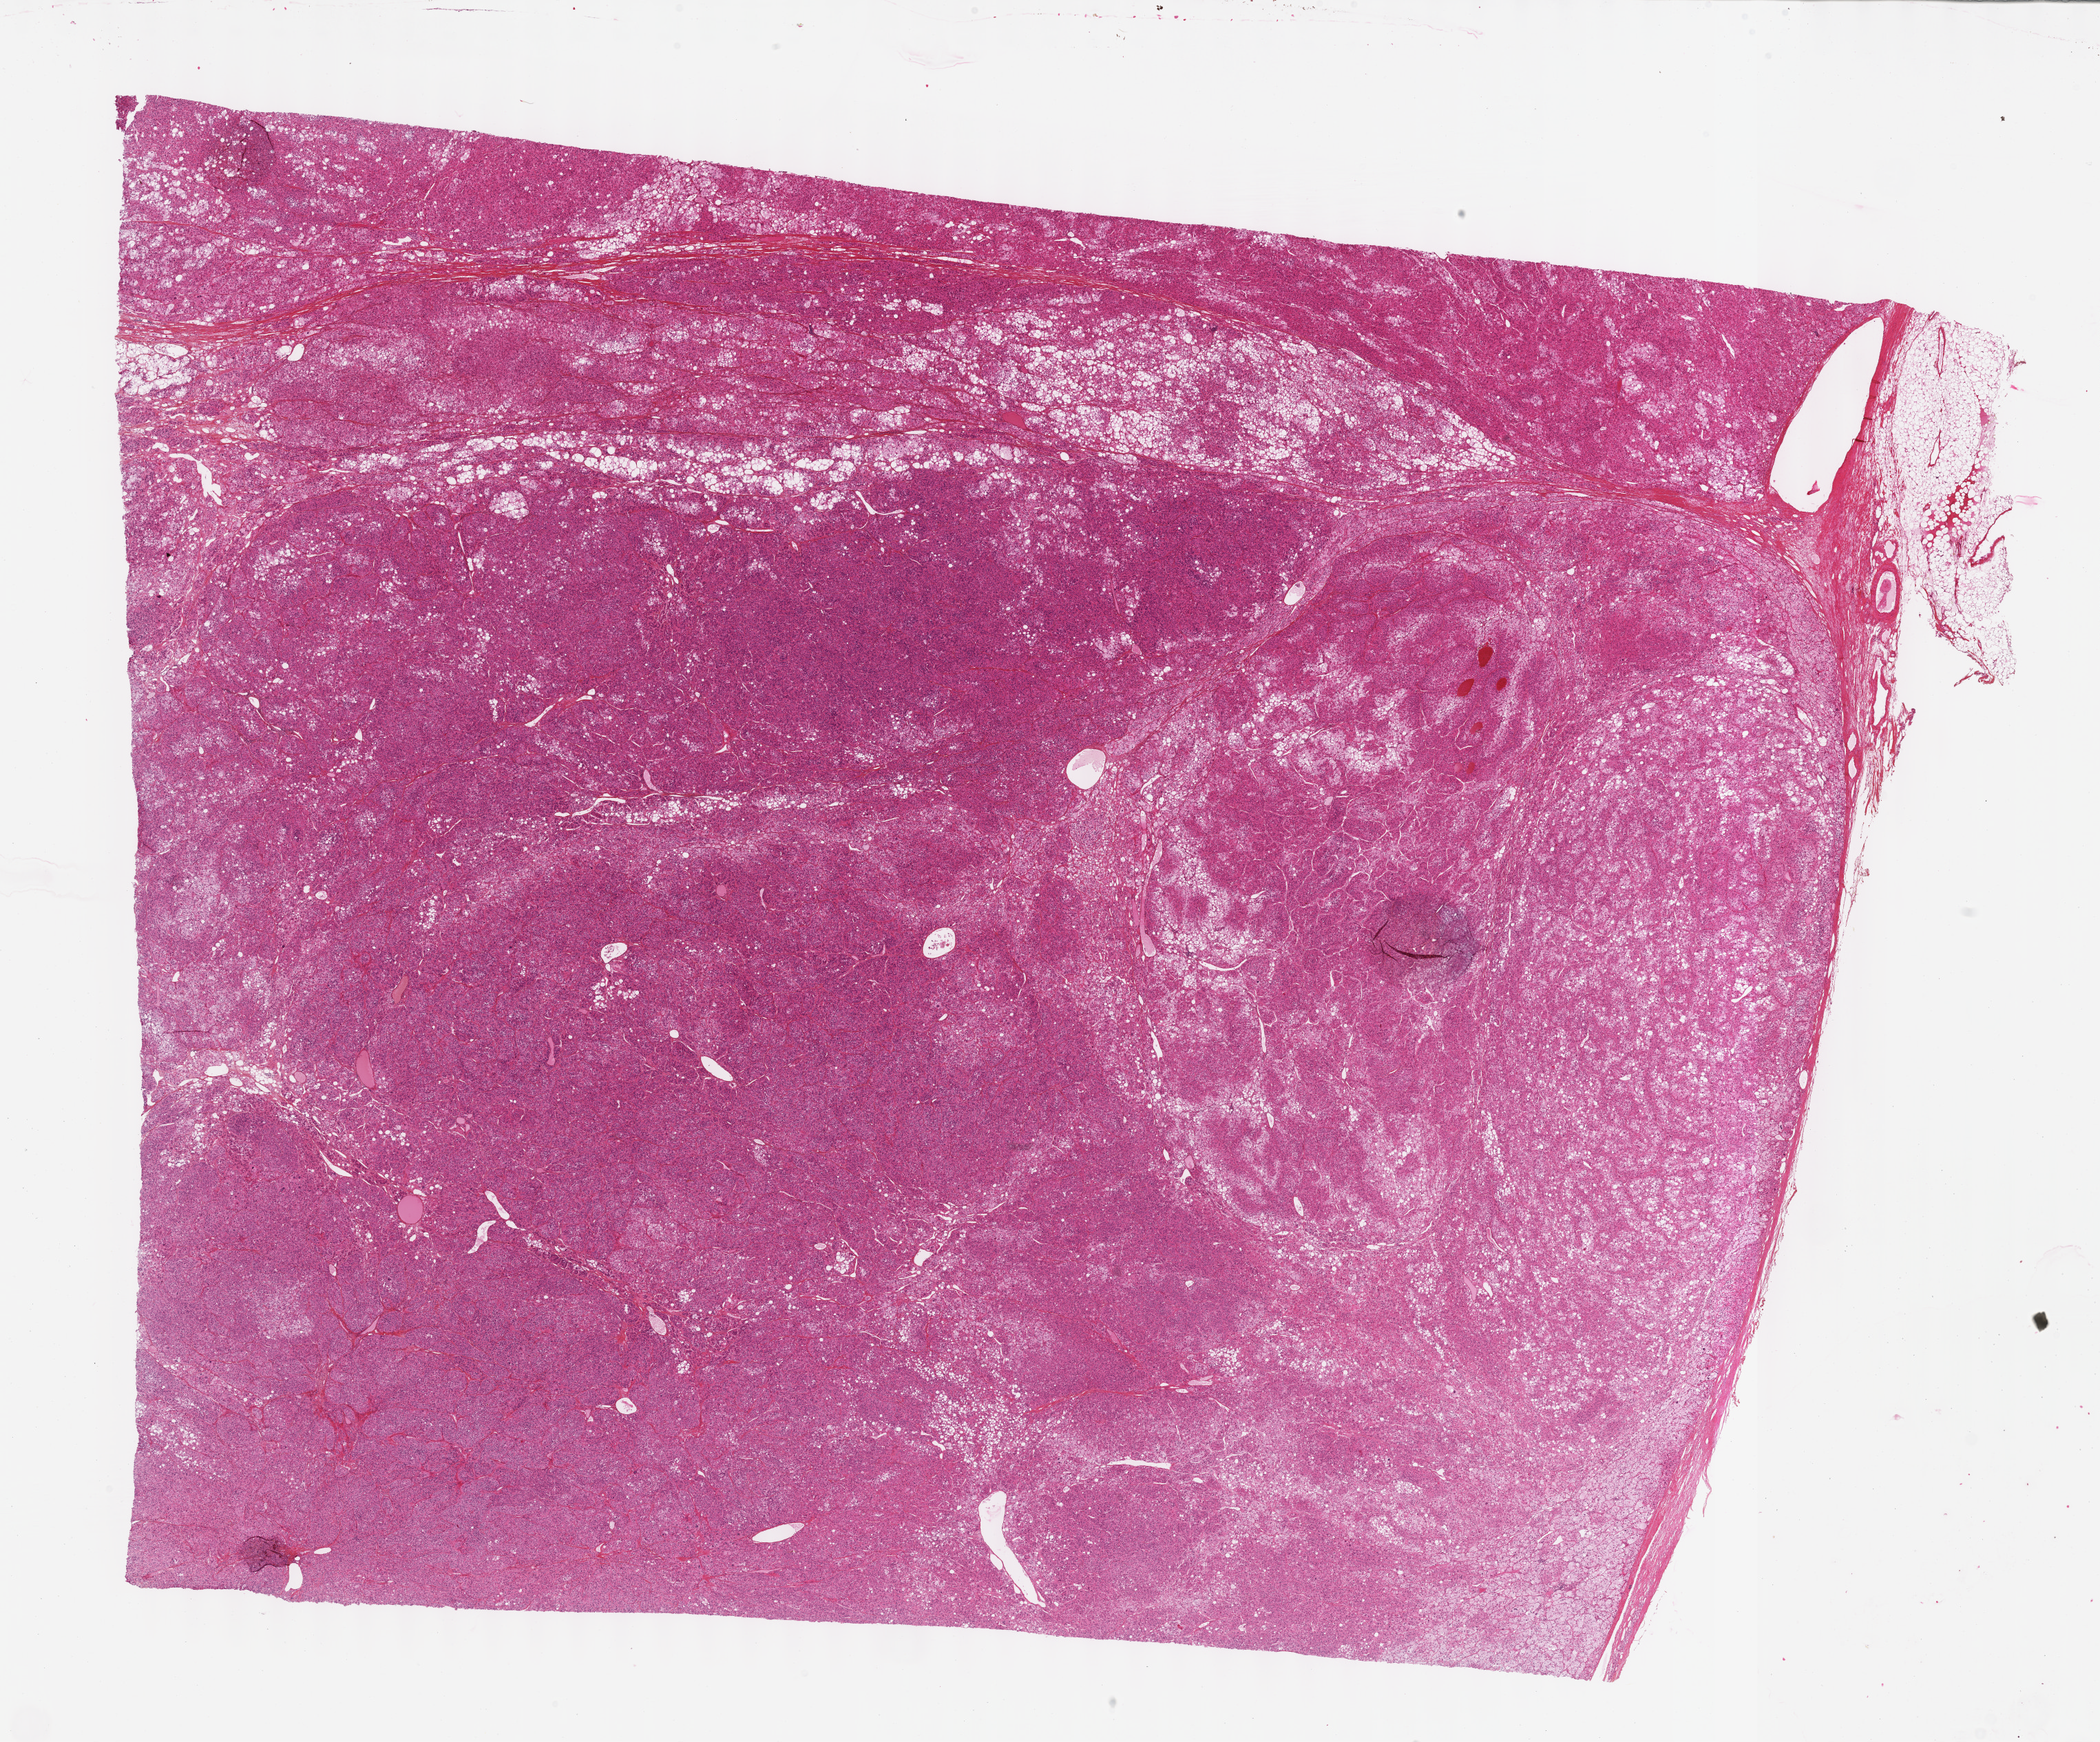
H&E whole-slide image — low-resolution overview of the scanned area, about 24.6 x 20.4 mm (slide scanned at 40x), formalin-fixed paraffin-embedded (FFPE) diagnostic section, primary tumour sample from the adrenal cortex. Patient: female, age at initial diagnosis 75 years.
Diagnosis: Adrenal cortical carcinoma.